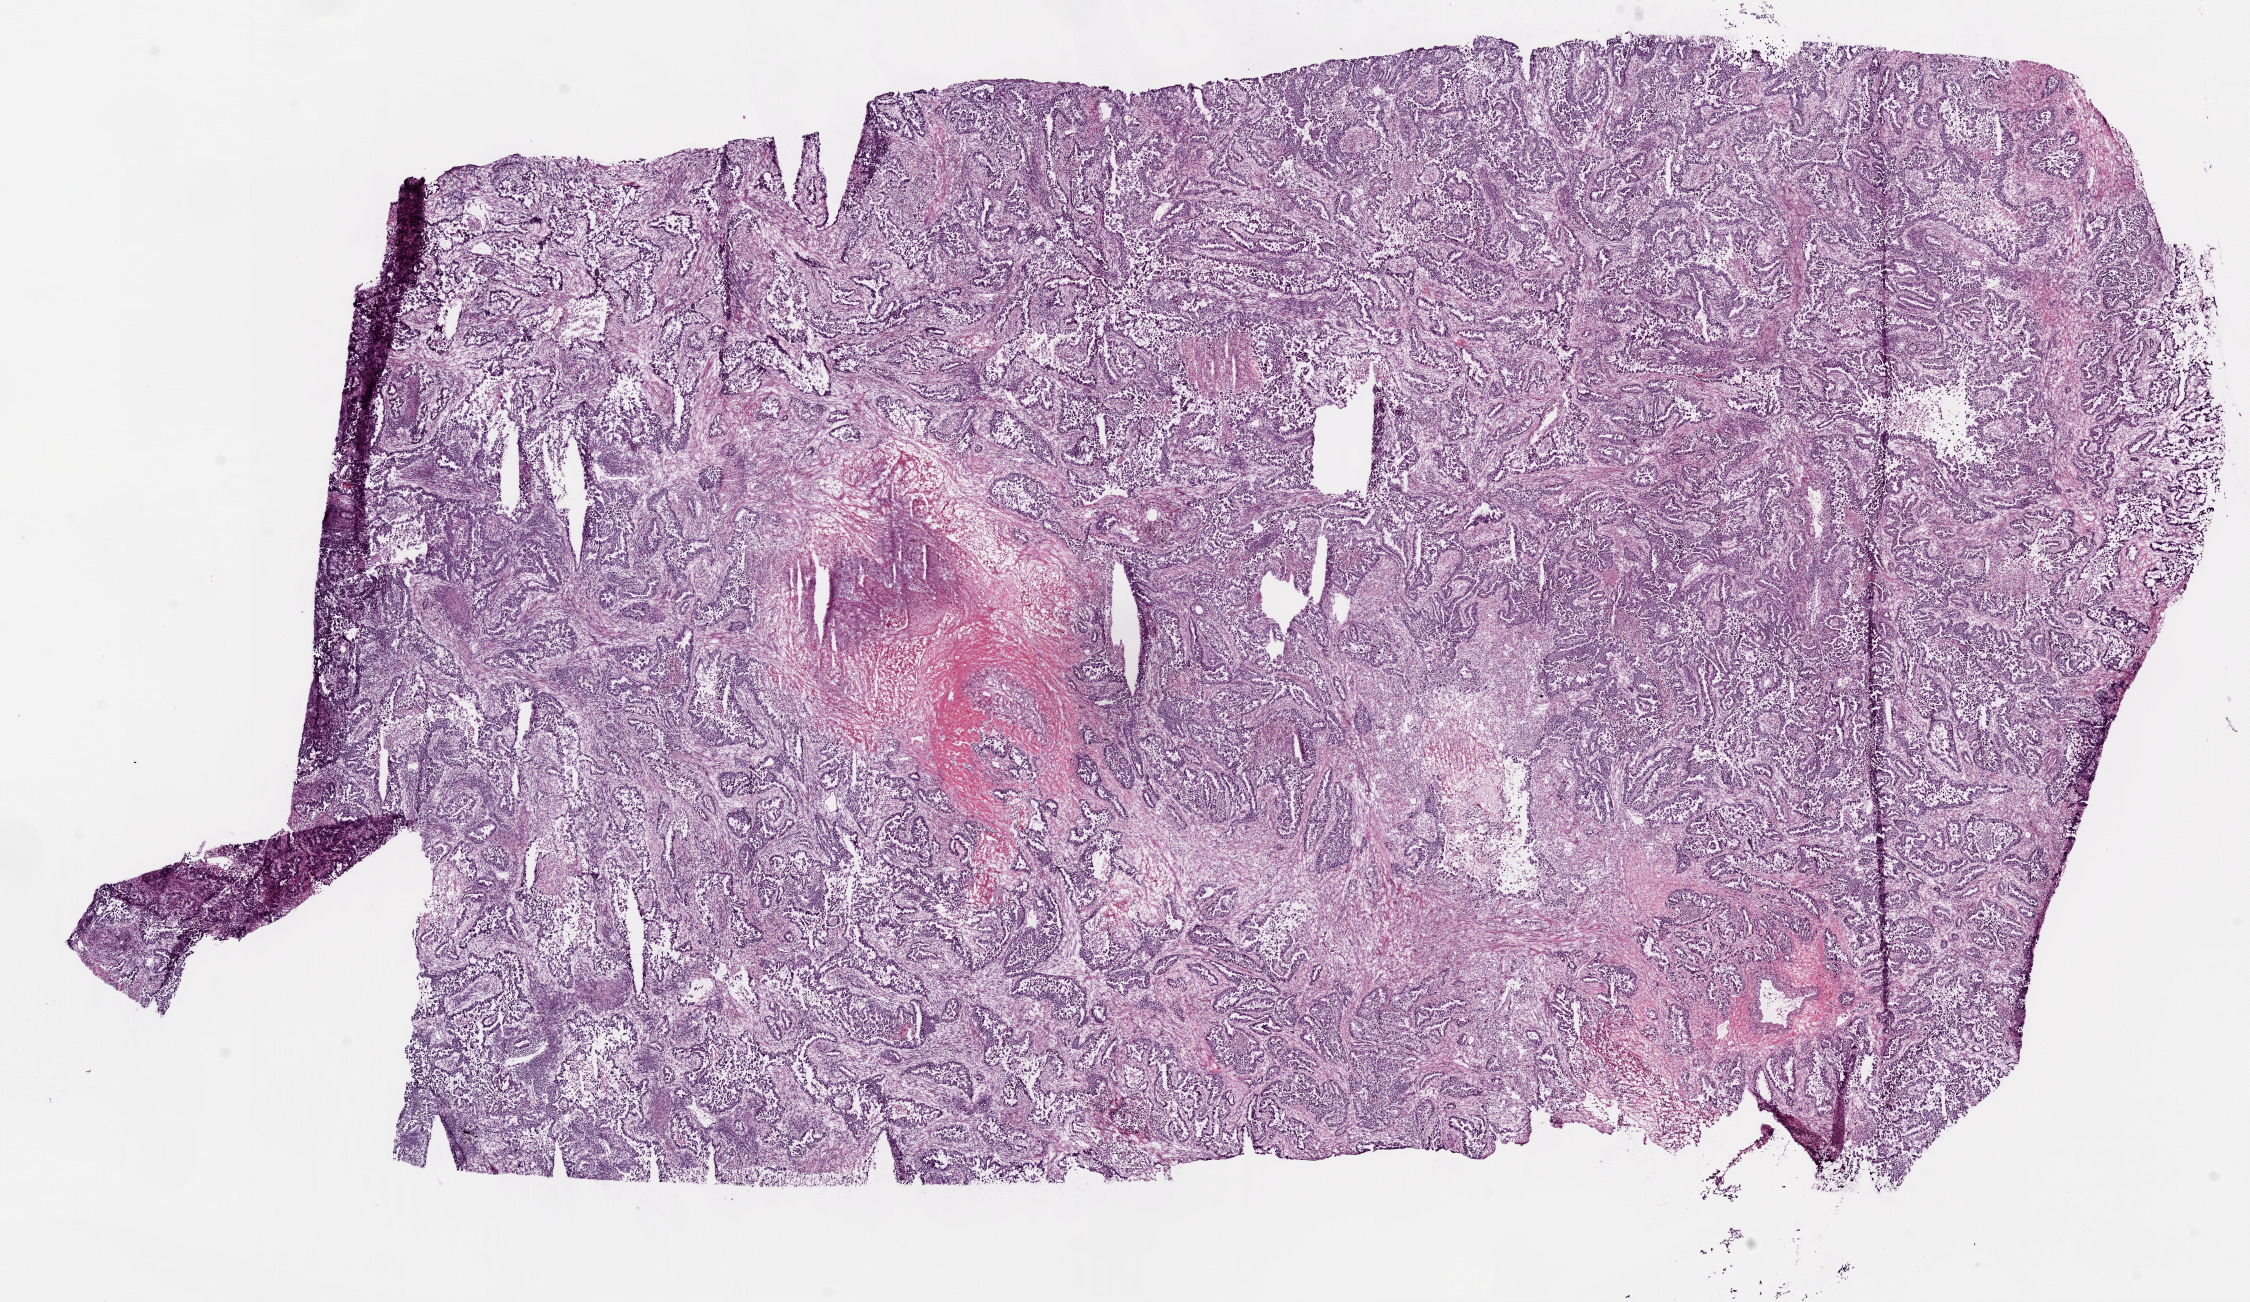
Whole-slide histology image, H&E, shown as a low-resolution overview of the whole scanned area (about 18.1 x 10.4 mm). Frozen section from the bottom of the tissue portion. Lung, primary tumour sample. Female, age 58 years at initial diagnosis. Pathologist review of this section (percent, as recorded): tumour cells 65%, tumour nuclei 75%, normal cells 0%, stromal cells 25%, necrosis 10%. Inflammatory infiltration, as recorded: lymphocyte infiltration 12%.
Laterality: right. AJCC pathologic stage: IB. Diagnosis: Adenocarcinoma with mixed subtypes (upper lobe, lung).